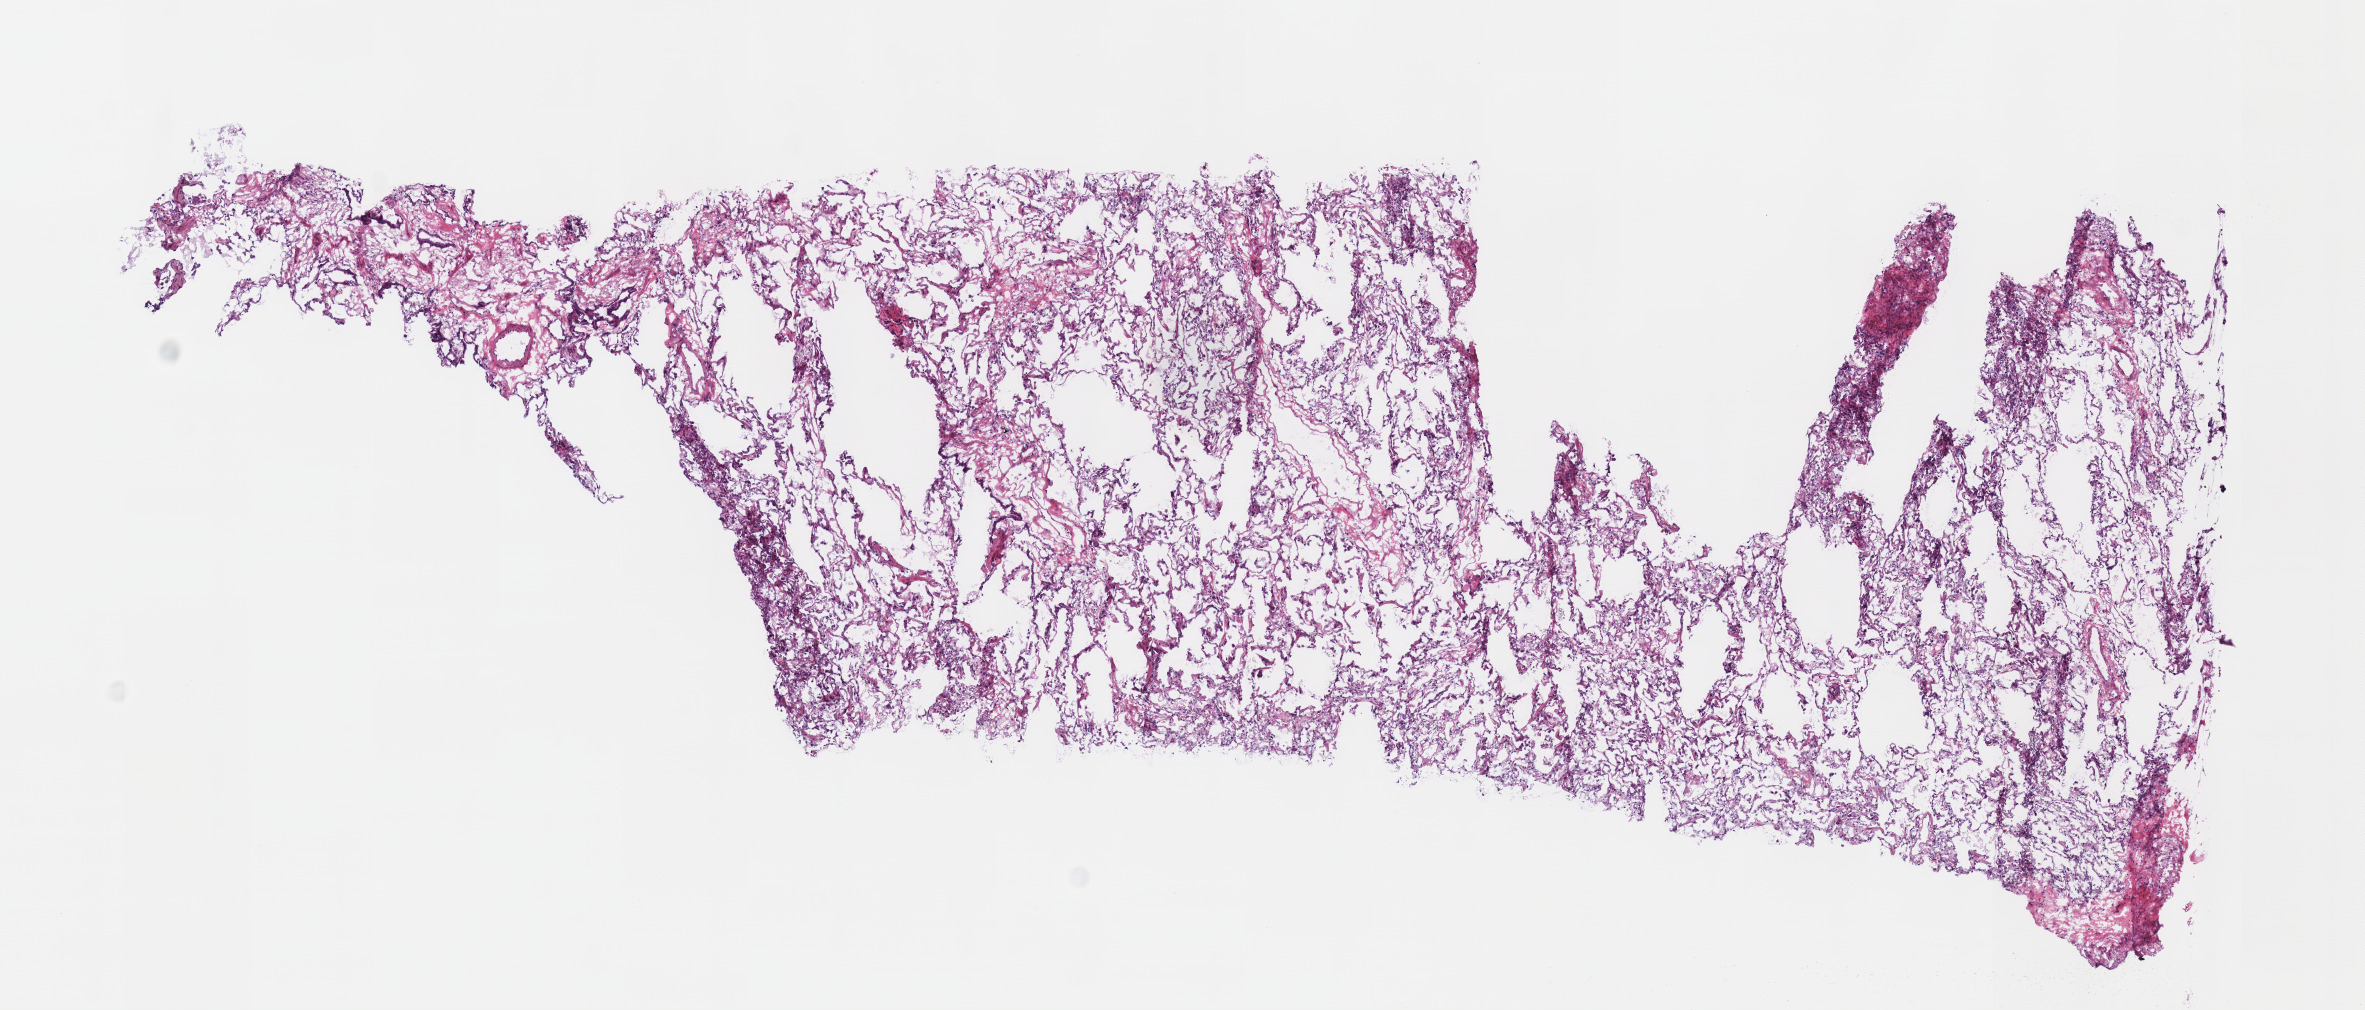
Whole-slide histology image, H&E-stained — a low-resolution overview of the entire scanned area, about 9.3 x 4.0 mm (from a 40x scan), frozen section, lung, solid tissue normal (non-tumour tissue) sample. Patient: male, age at initial diagnosis 71 years.
This section: solid tissue normal sample (biorepository sample class). Patient diagnosis: Squamous cell carcinoma, NOS (upper lobe, lung).